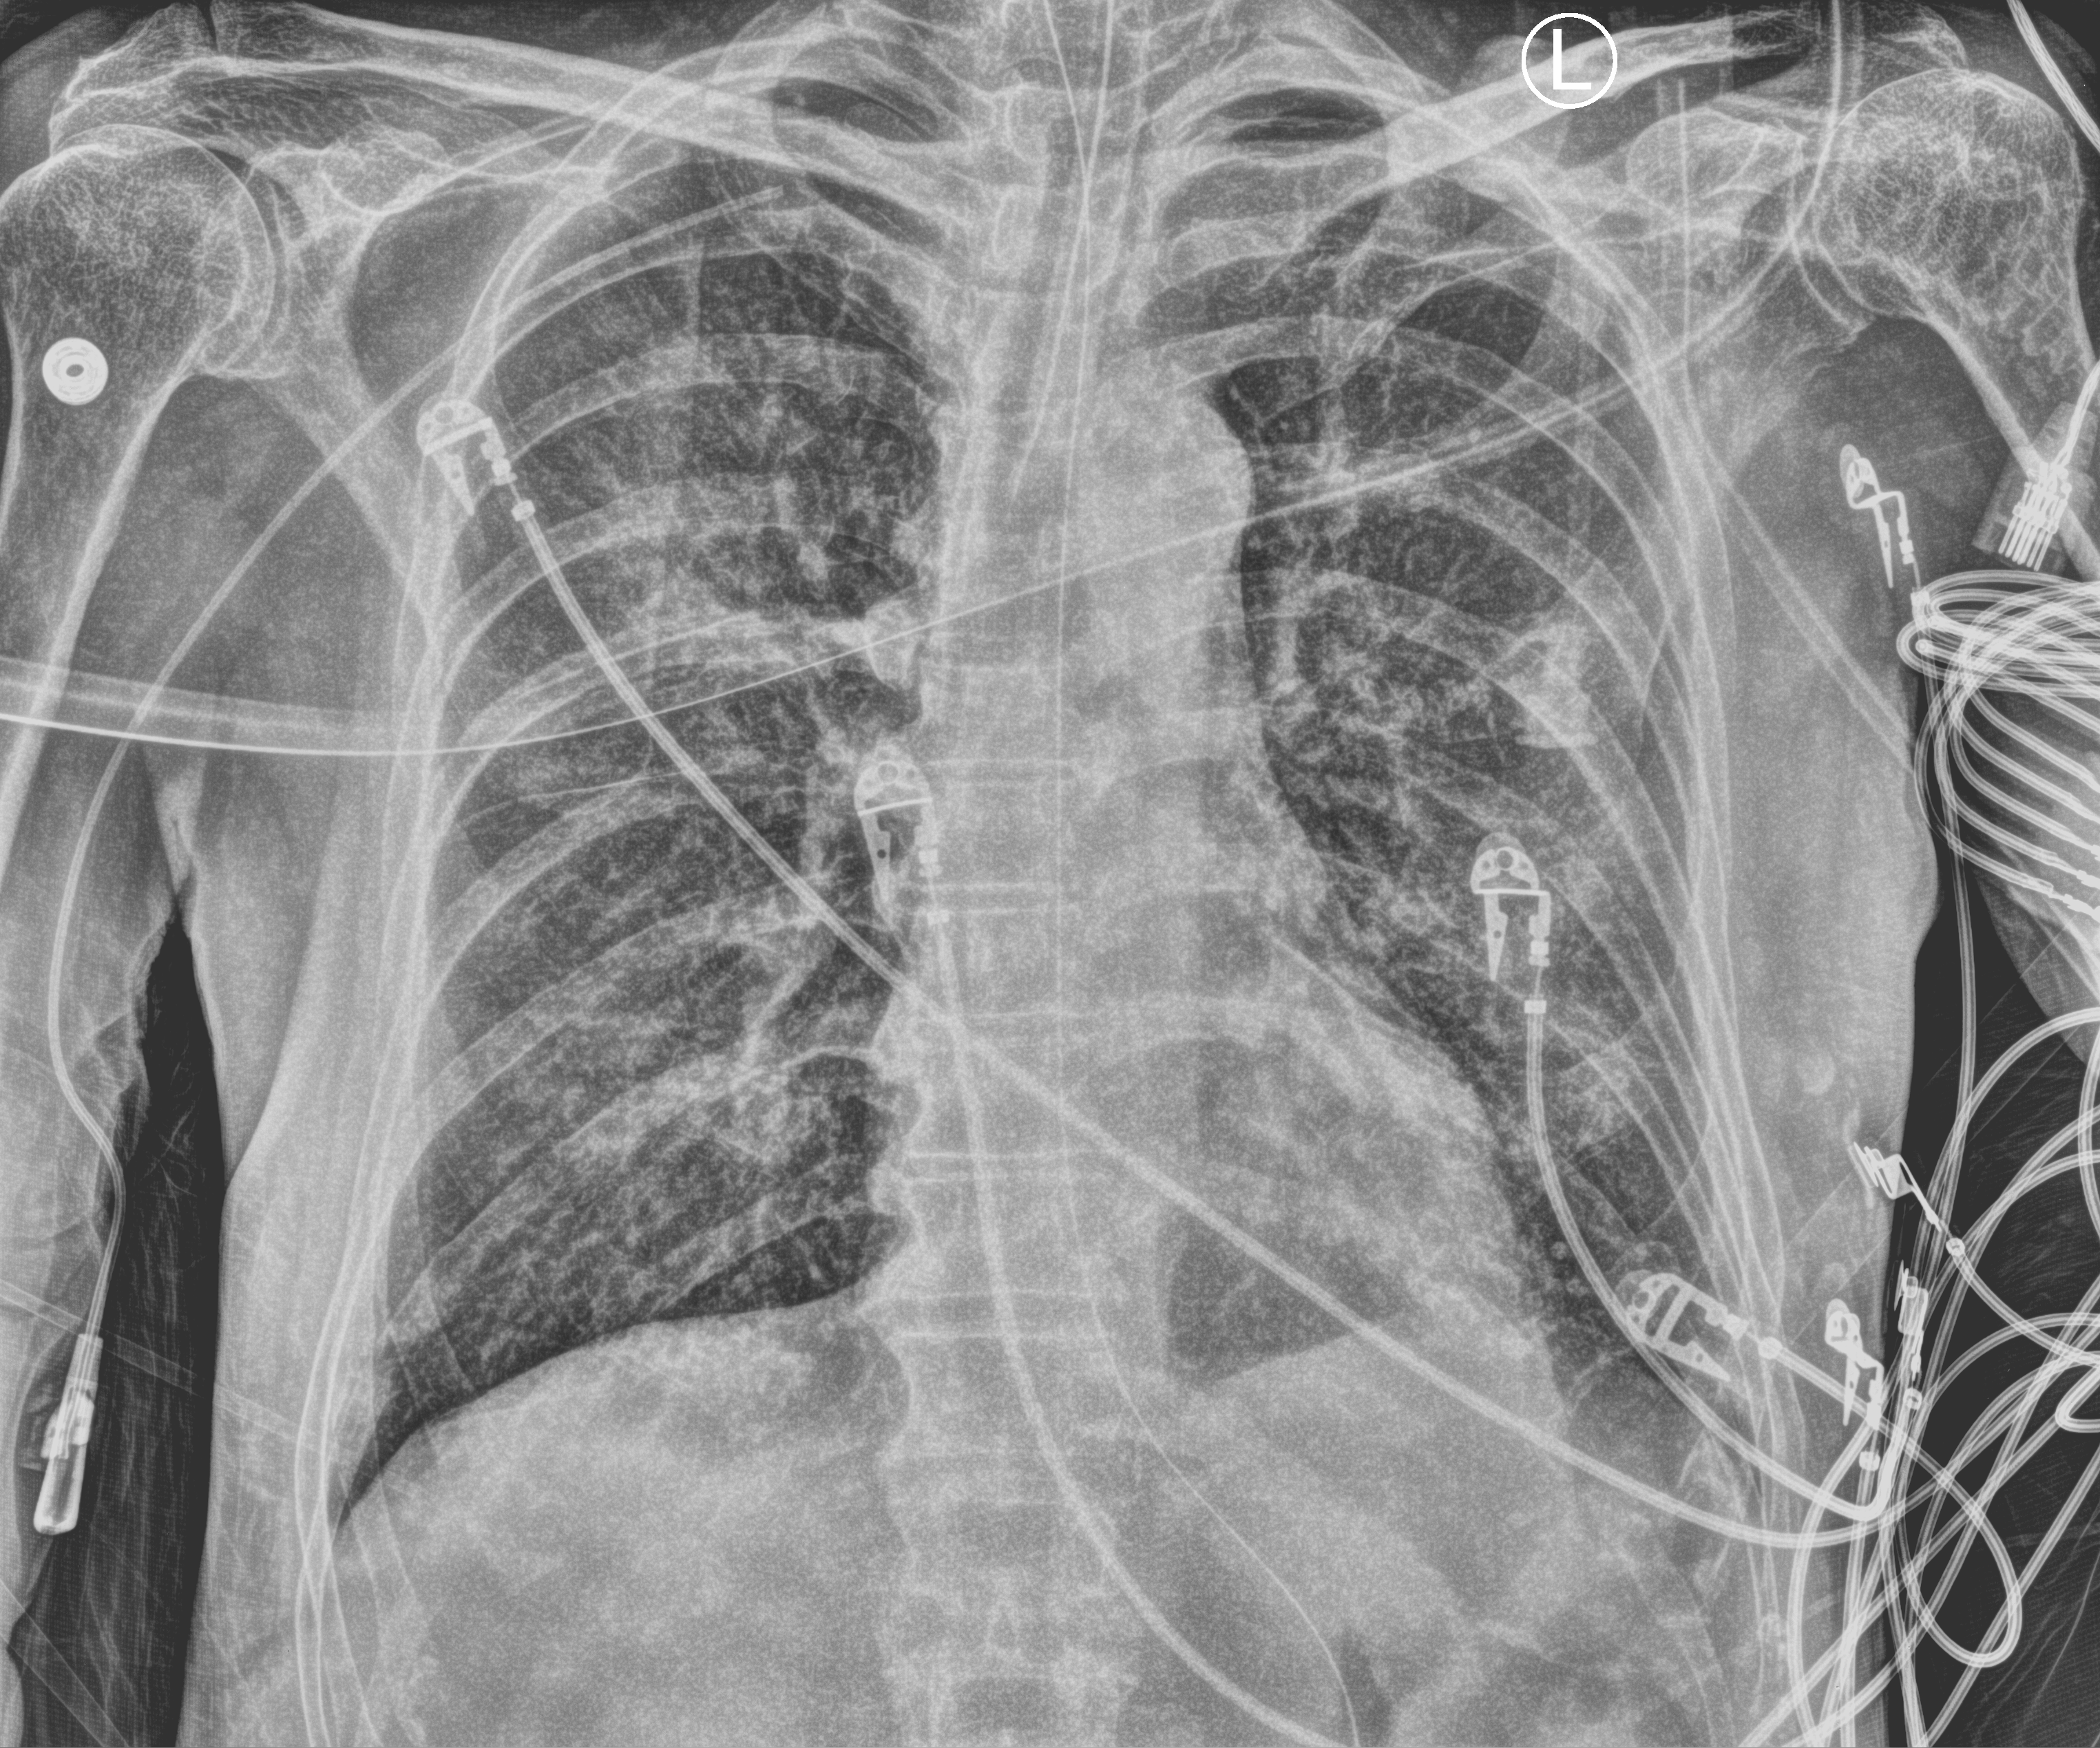
Portable chest radiograph; anteroposterior (AP) projection. Patient hospitalised with COVID-19; male, aged 60–74 years.
Admission-level facts for this patient (not findings on this image; timing relative to this image not recorded):
- mechanically ventilated during this hospital stay: yes